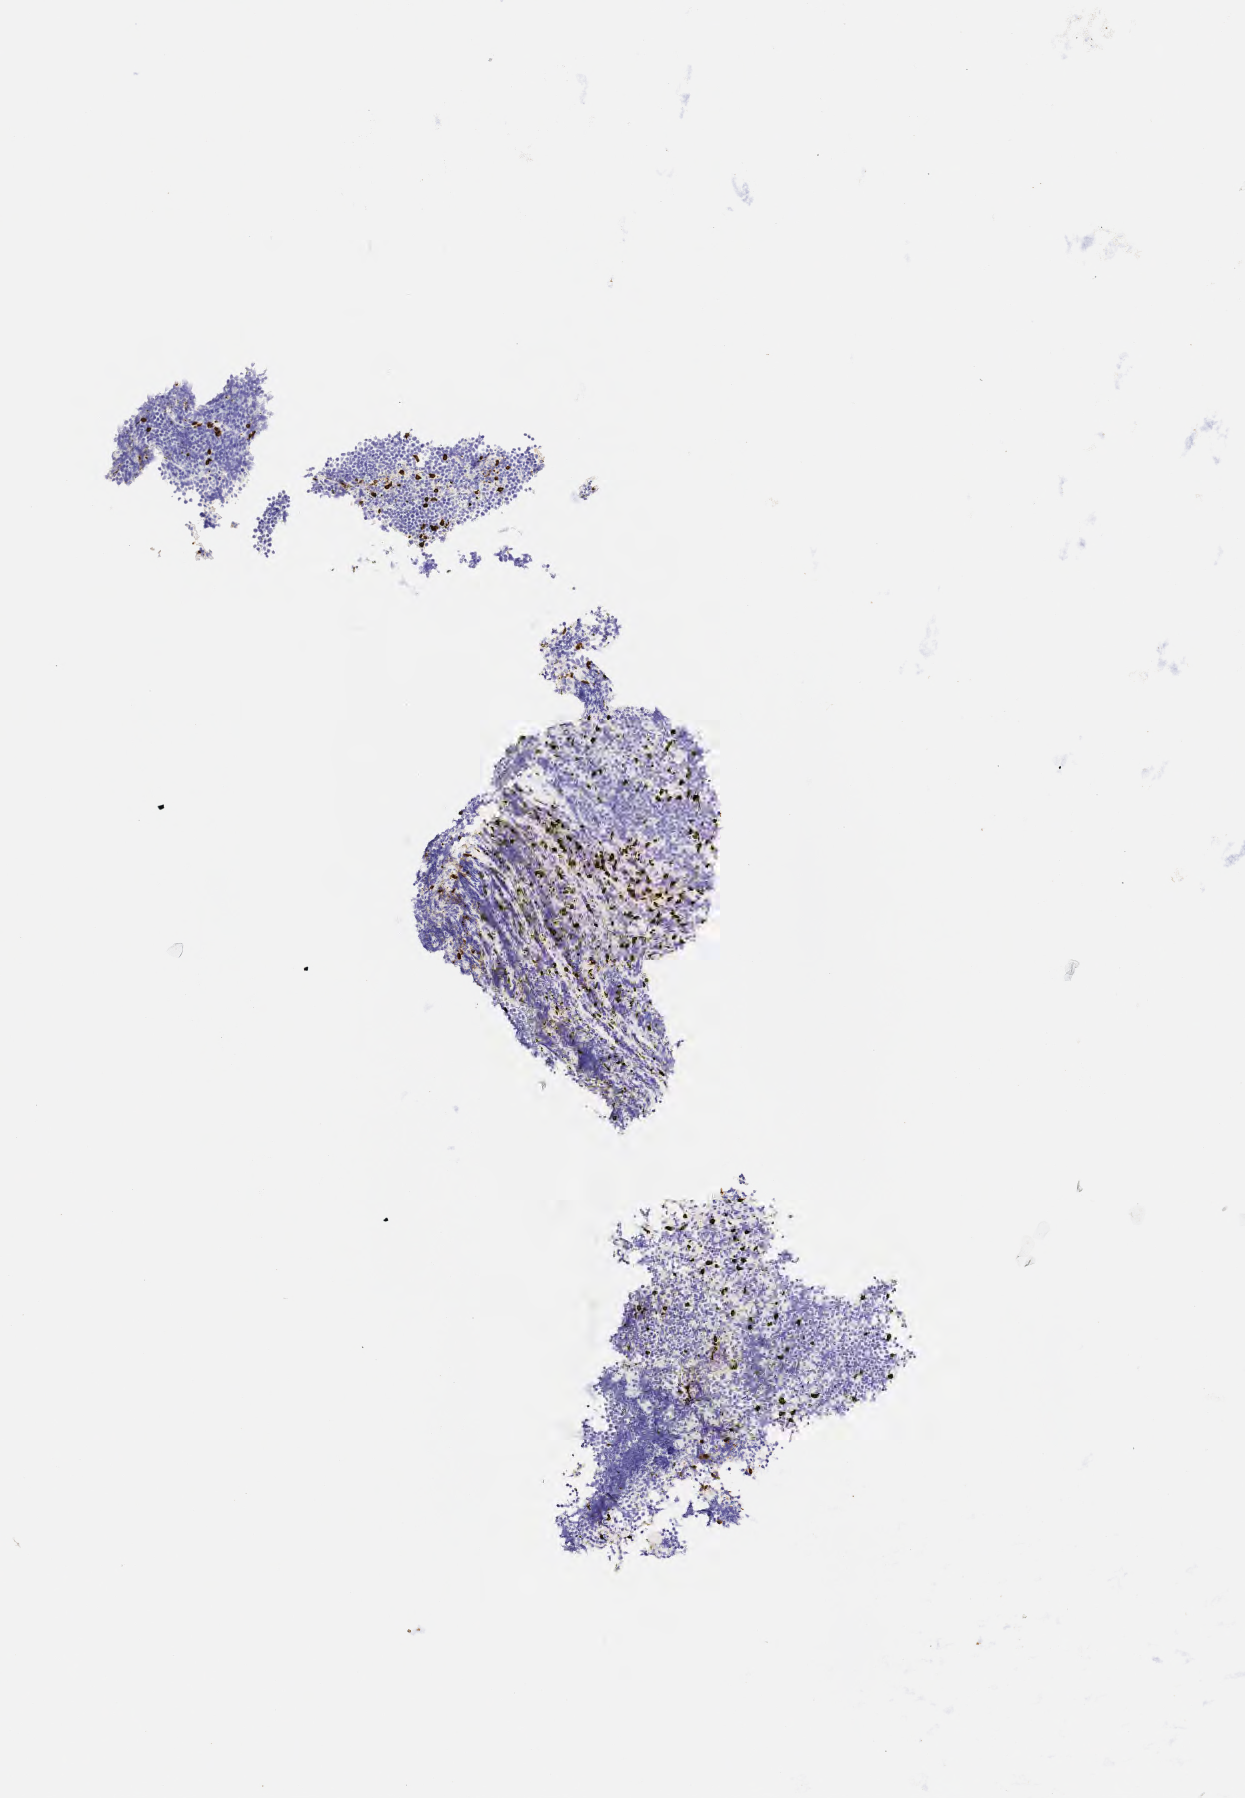
IHC for CD3, whole-slide image — low-resolution overview of the scanned area, about 2.5 x 3.6 mm; tumor tissue; anatomic site: abdomen proper. Male patient; age at initial diagnosis 6 years.
• histologic diagnosis: Burkitt lymphoma, NOS